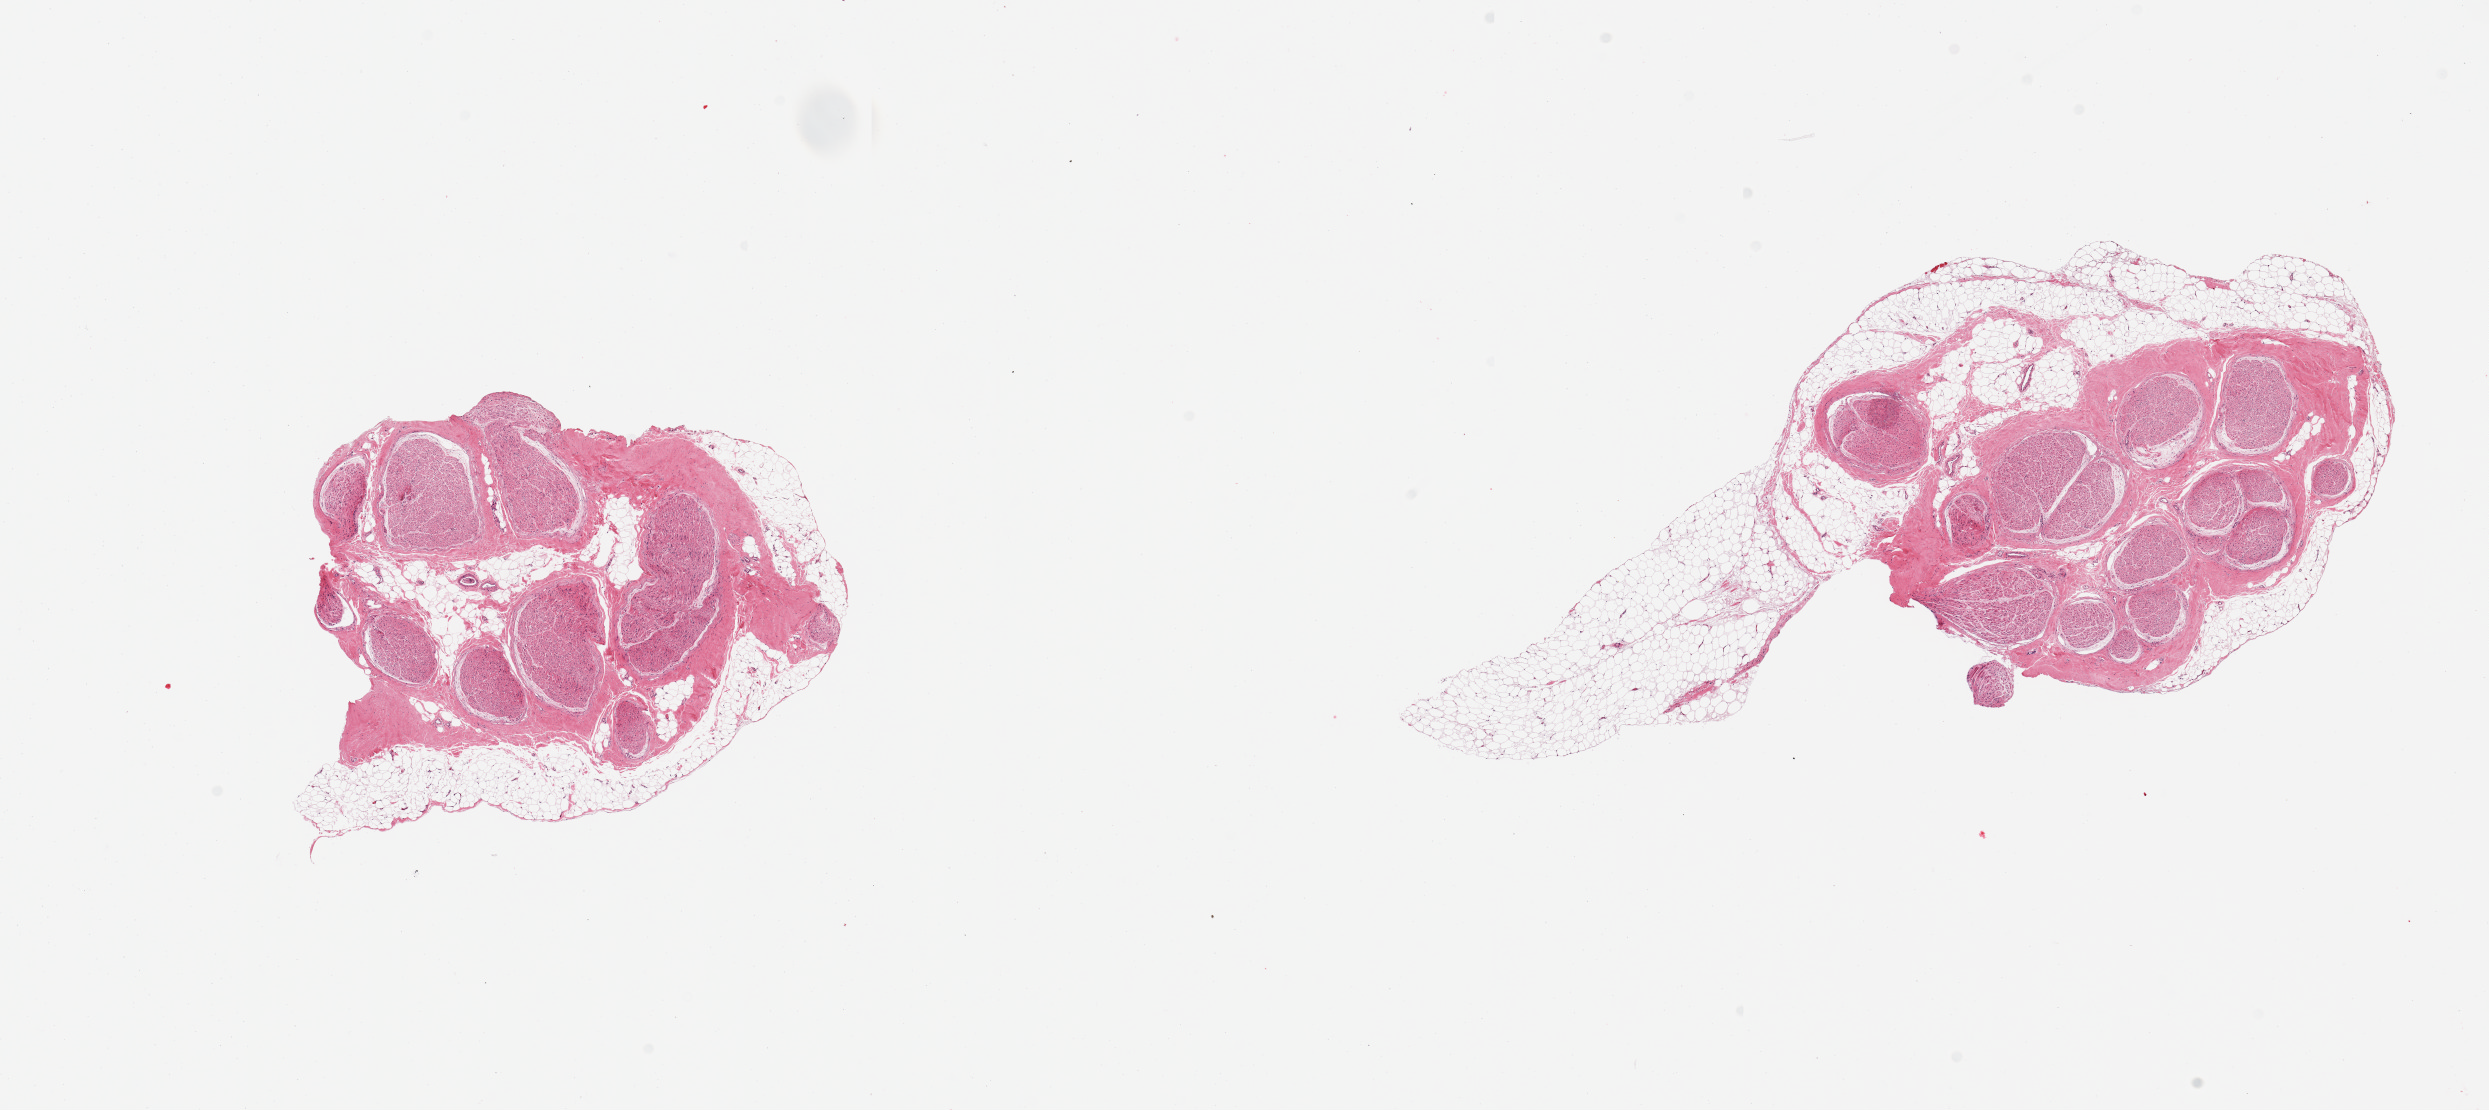
Digitized haematoxylin and eosin-stained section, shown as a low-resolution overview of the whole scanned area (about 19.7 x 8.8 mm). PAXgene-fixed, paraffin-embedded tissue. Target tissue: tibial nerve. Tissue donor sample. Donor: male.
Pathologist's review note for this sample: 2 pieces; 40% external fat on 1, 30% internal & external fat on other.